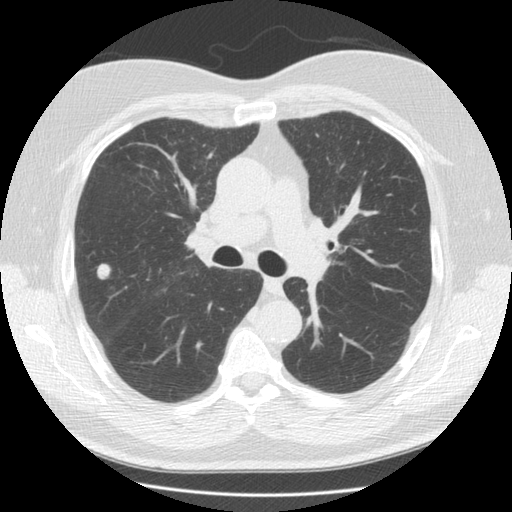
Low-dose screening chest CT, one axial slice. Position 89 of 146 along the scan axis. 120 kVp. Lung window (W 1500 / L -600 HU). 2.5 mm slice thickness. 512 × 512 image matrix, field of view 350 × 350 mm.
Outlined on this slice (manually delineated by an expert):
- lesion 1 (tumor, upper lobe of right lung): bounding box [x1, y1, x2, y2] px = [97, 263, 111, 280]